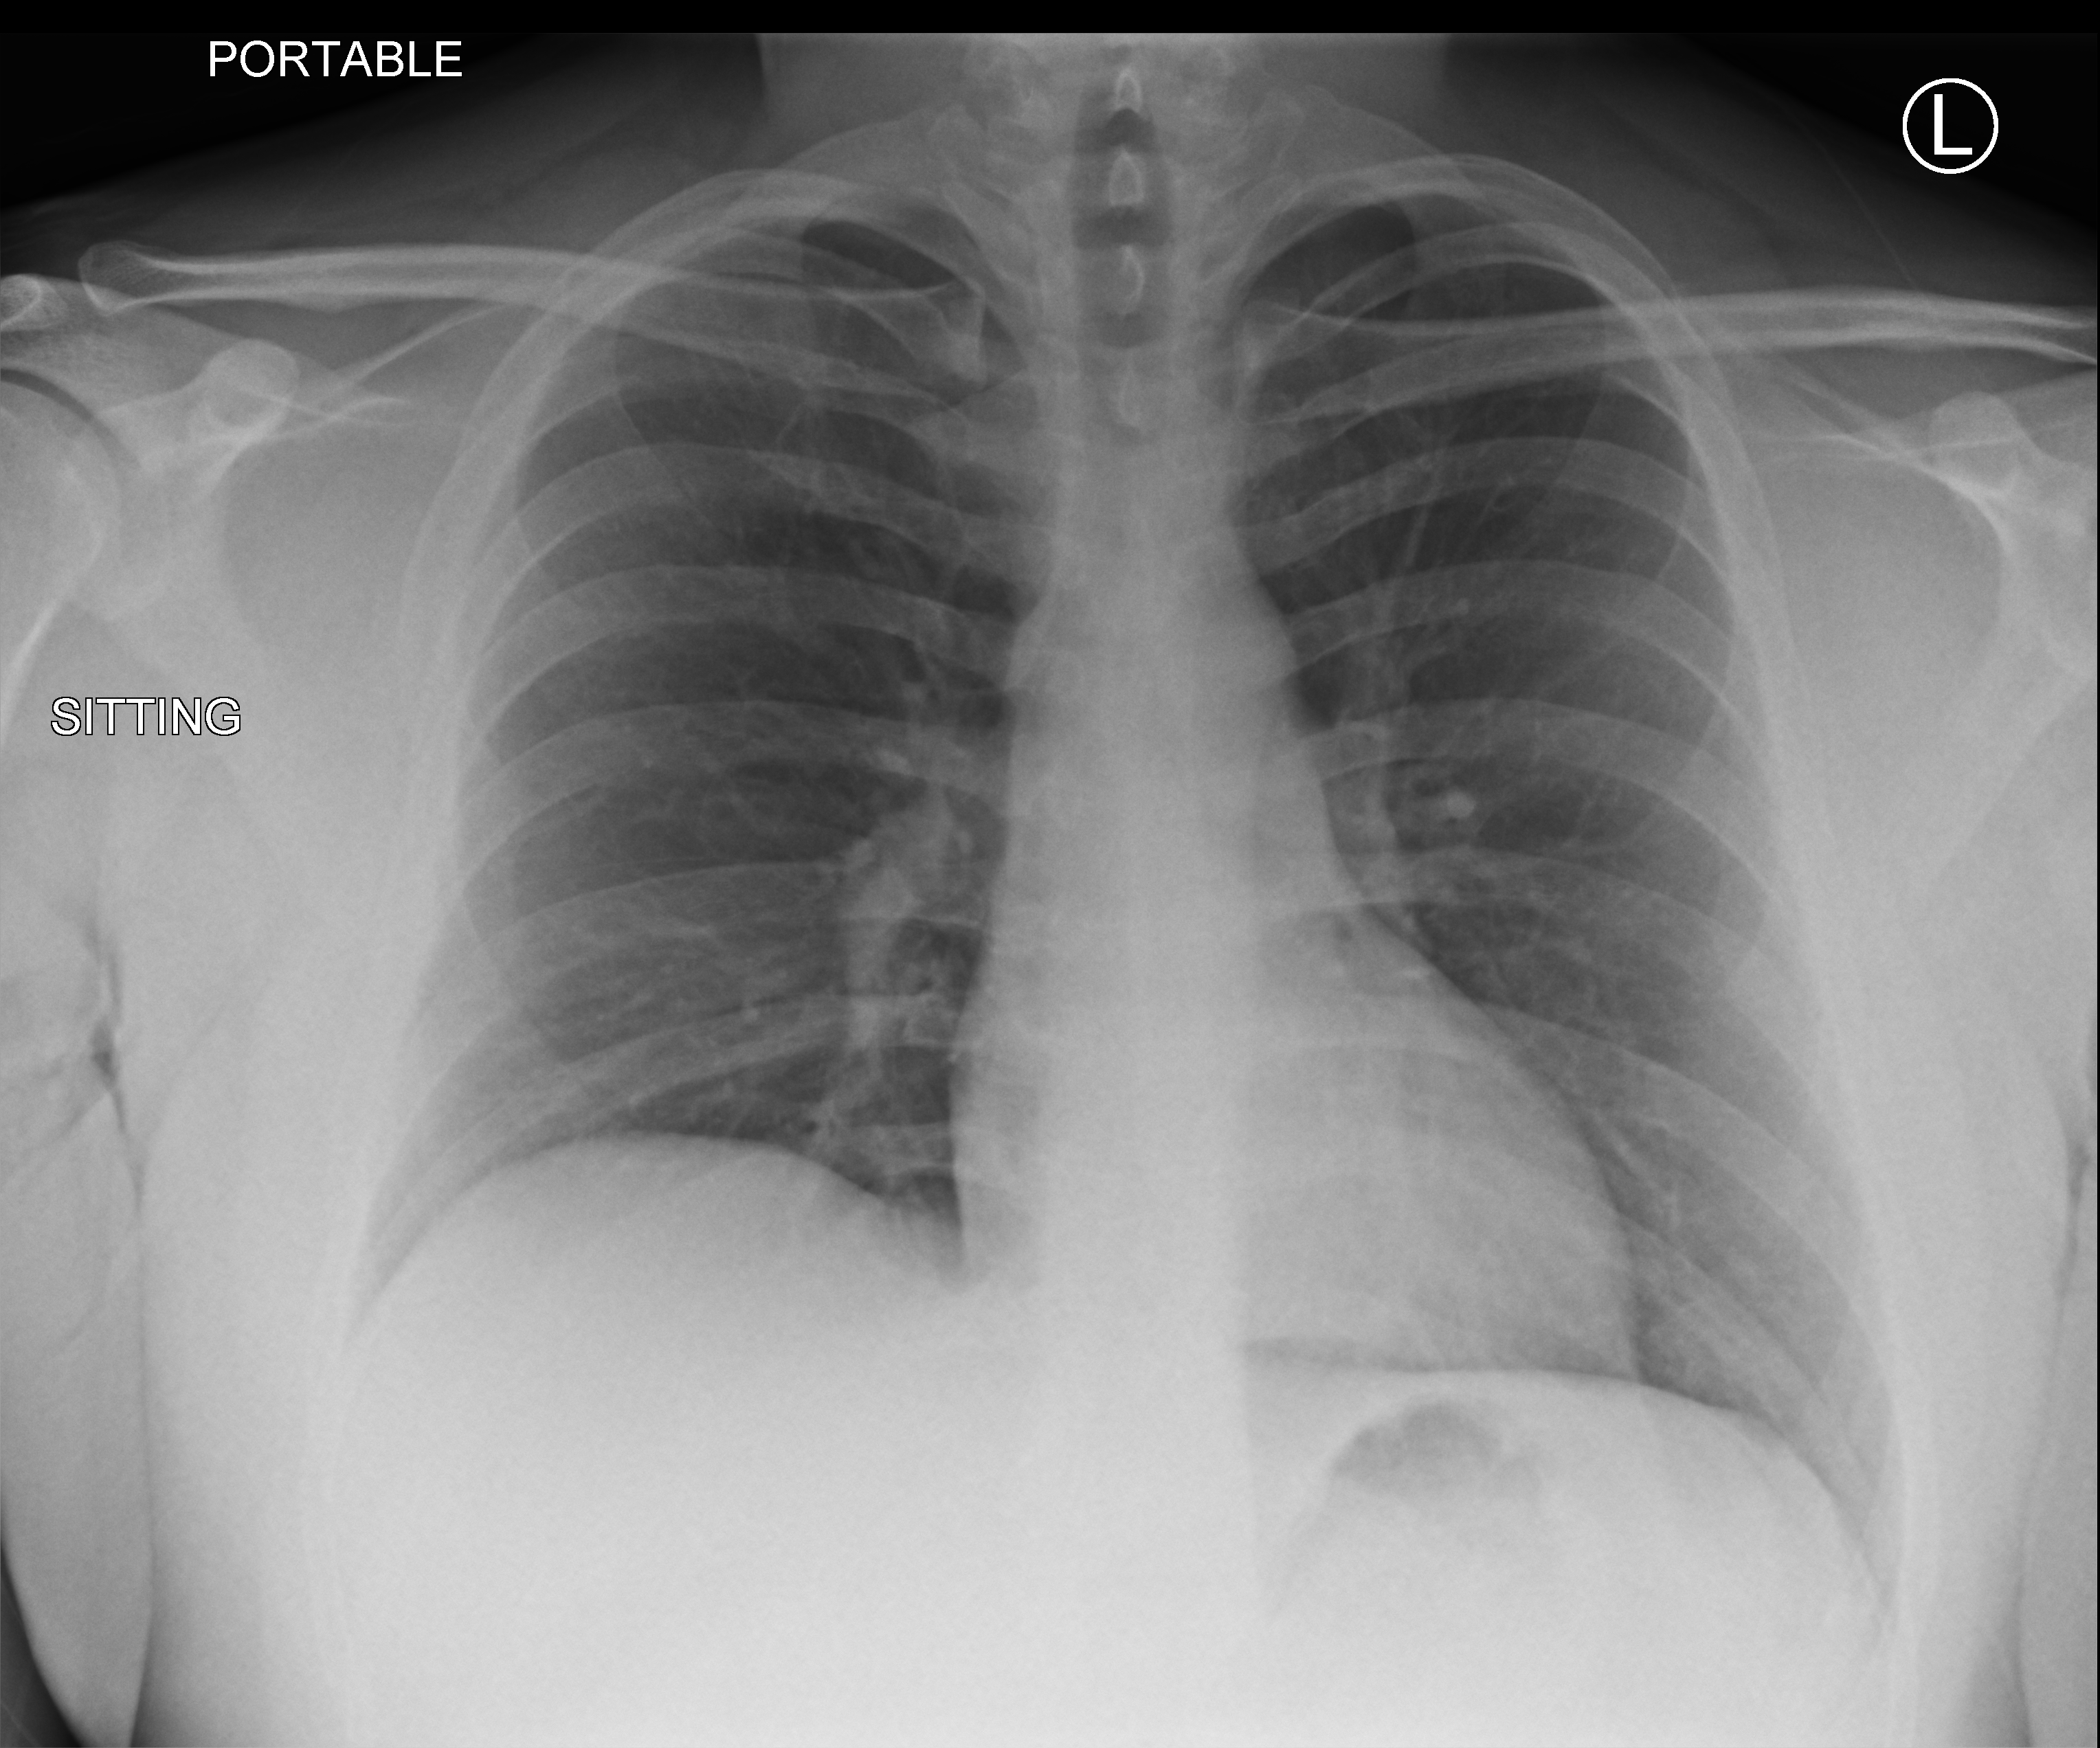
Chest X-ray (portable). Patient hospitalised with COVID-19; male, aged 18–59 years.
From the hospital-stay record, not from the radiograph (when in the stay this image was taken is not recorded):
- other chronic lung disease (admission record): yes
- chronic kidney disease (admission record): no
- admitted to intensive care during this hospital stay: no